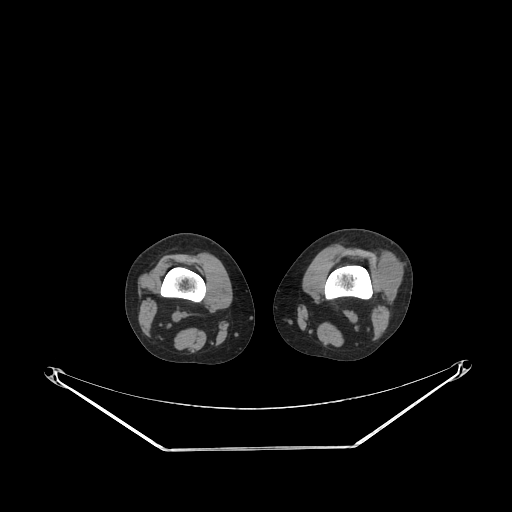
CT of an extremity soft-tissue mass (from a PET/CT study), one axial slice. Slice 172 of 223 in the series (ordered by position). Reconstruction kernel STANDARD. 140 kVp. Soft-tissue window (W 400 / L 40 HU). 512 × 512 image matrix, field of view 500 × 500 mm. Female patient. From the clinical record (not read from this slice): histological type: spindle cell suggestive of biphasic synovial sarcoma; grade: intermediate; site of the primary tumour: left knee.
Structures marked on this image (expert contour drawn on MRI and transferred to this co-registered scan by the dataset authors):
- gross tumour volume including surrounding oedema: box from (x=374, y=251) to (x=401, y=298) px
- gross tumour volume (mass): (x=374, y=253)–(x=401, y=298)